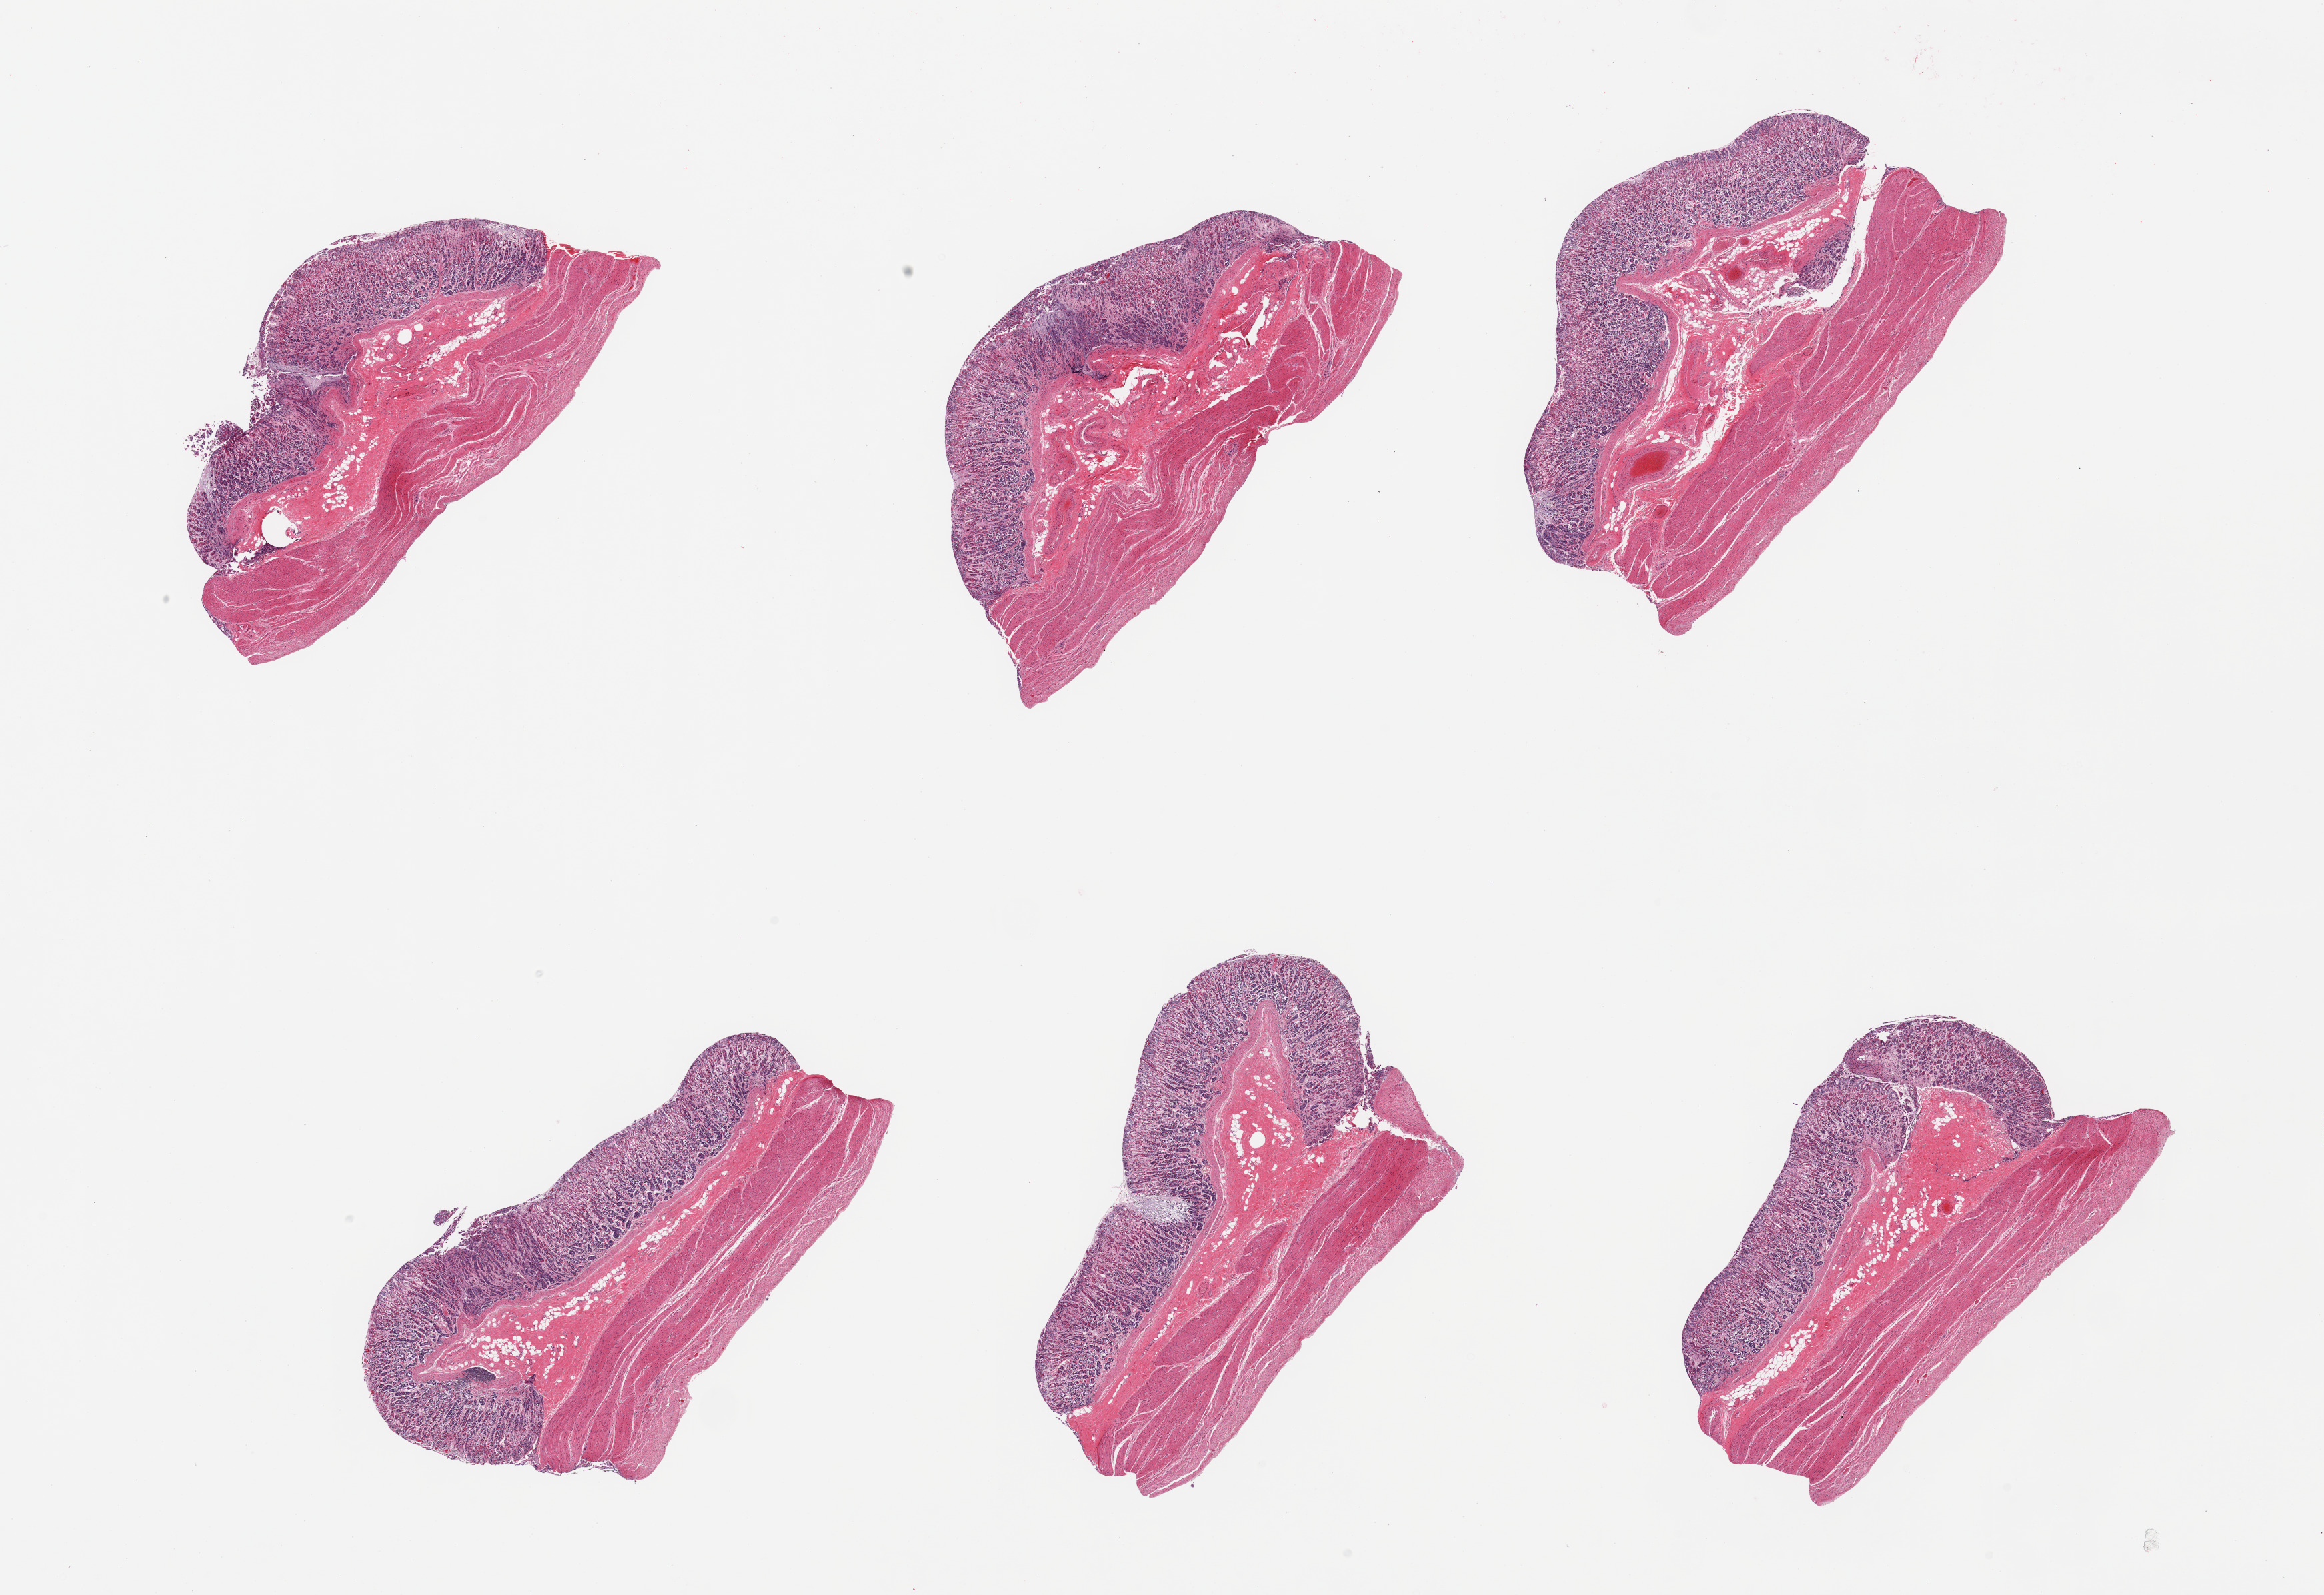
Whole-slide image, H&E stain, brightfield — low-resolution overview of the scanned area, about 27.6 x 18.9 mm; PAXgene-fixed, paraffin-embedded tissue; sampled site (target tissue): stomach; tissue donor sample.
Pathologist's review note for this sample: 6 pieces; mucosa=autolysis 2; muscle=1; congestion.